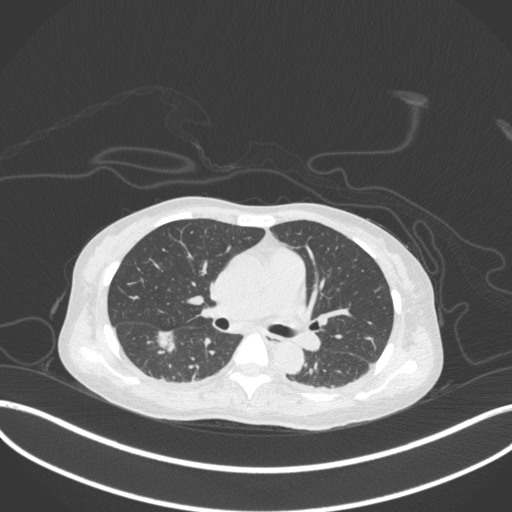
Chest CT, one axial slice; reconstruction kernel B31f; lung window (W 1500 / L -600 HU); 1 mm slice thickness; 512 × 512 image matrix, field of view 400 × 400 mm. Female patient, age 44 years. From the clinical record (not read from this slice): clinical TNM (as recorded): T1c N0 M0.
Structures marked on this image (rectangle marked by the reading radiologist):
- lung tumour (recorded histology: adenocarcinoma): bounding box <148,327,176,353> (left, top, right, bottom; pixels)